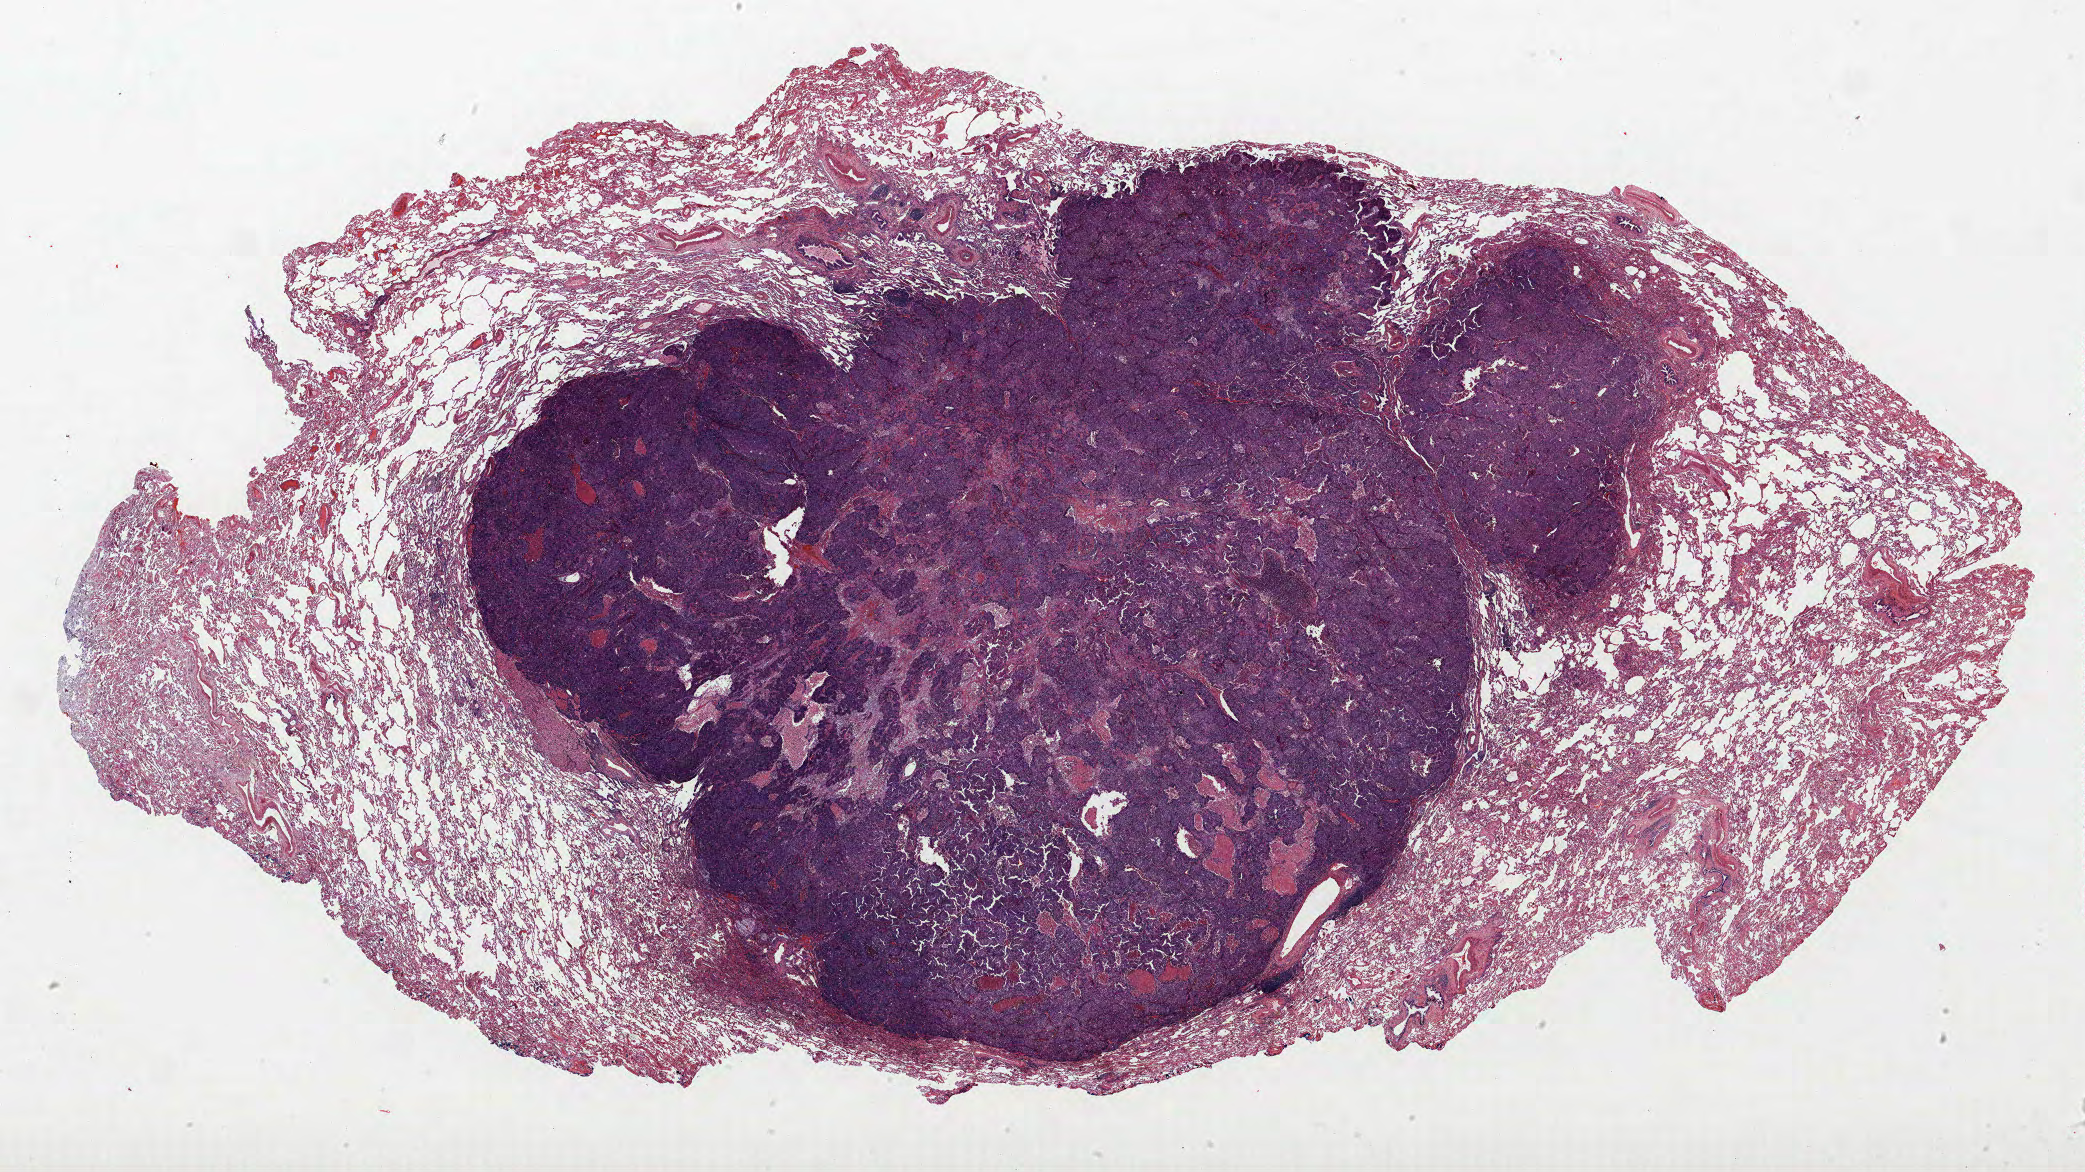
Hematoxylin and eosin (H&E) stained whole-slide image — low-resolution overview of the scanned area, about 33.4 x 18.8 mm, FFPE section, lung. Male patient, aged 56 at enrolment. Former smoker at enrolment. Grade: poorly differentiated (G3).
Primary tumour location (clinical record): right lower lobe. Tumour size (pathology): 24 mm. Stage (AJCC 6th edition): IA. Participant's lung-cancer diagnosis: Adenocarcinoma, NOS.